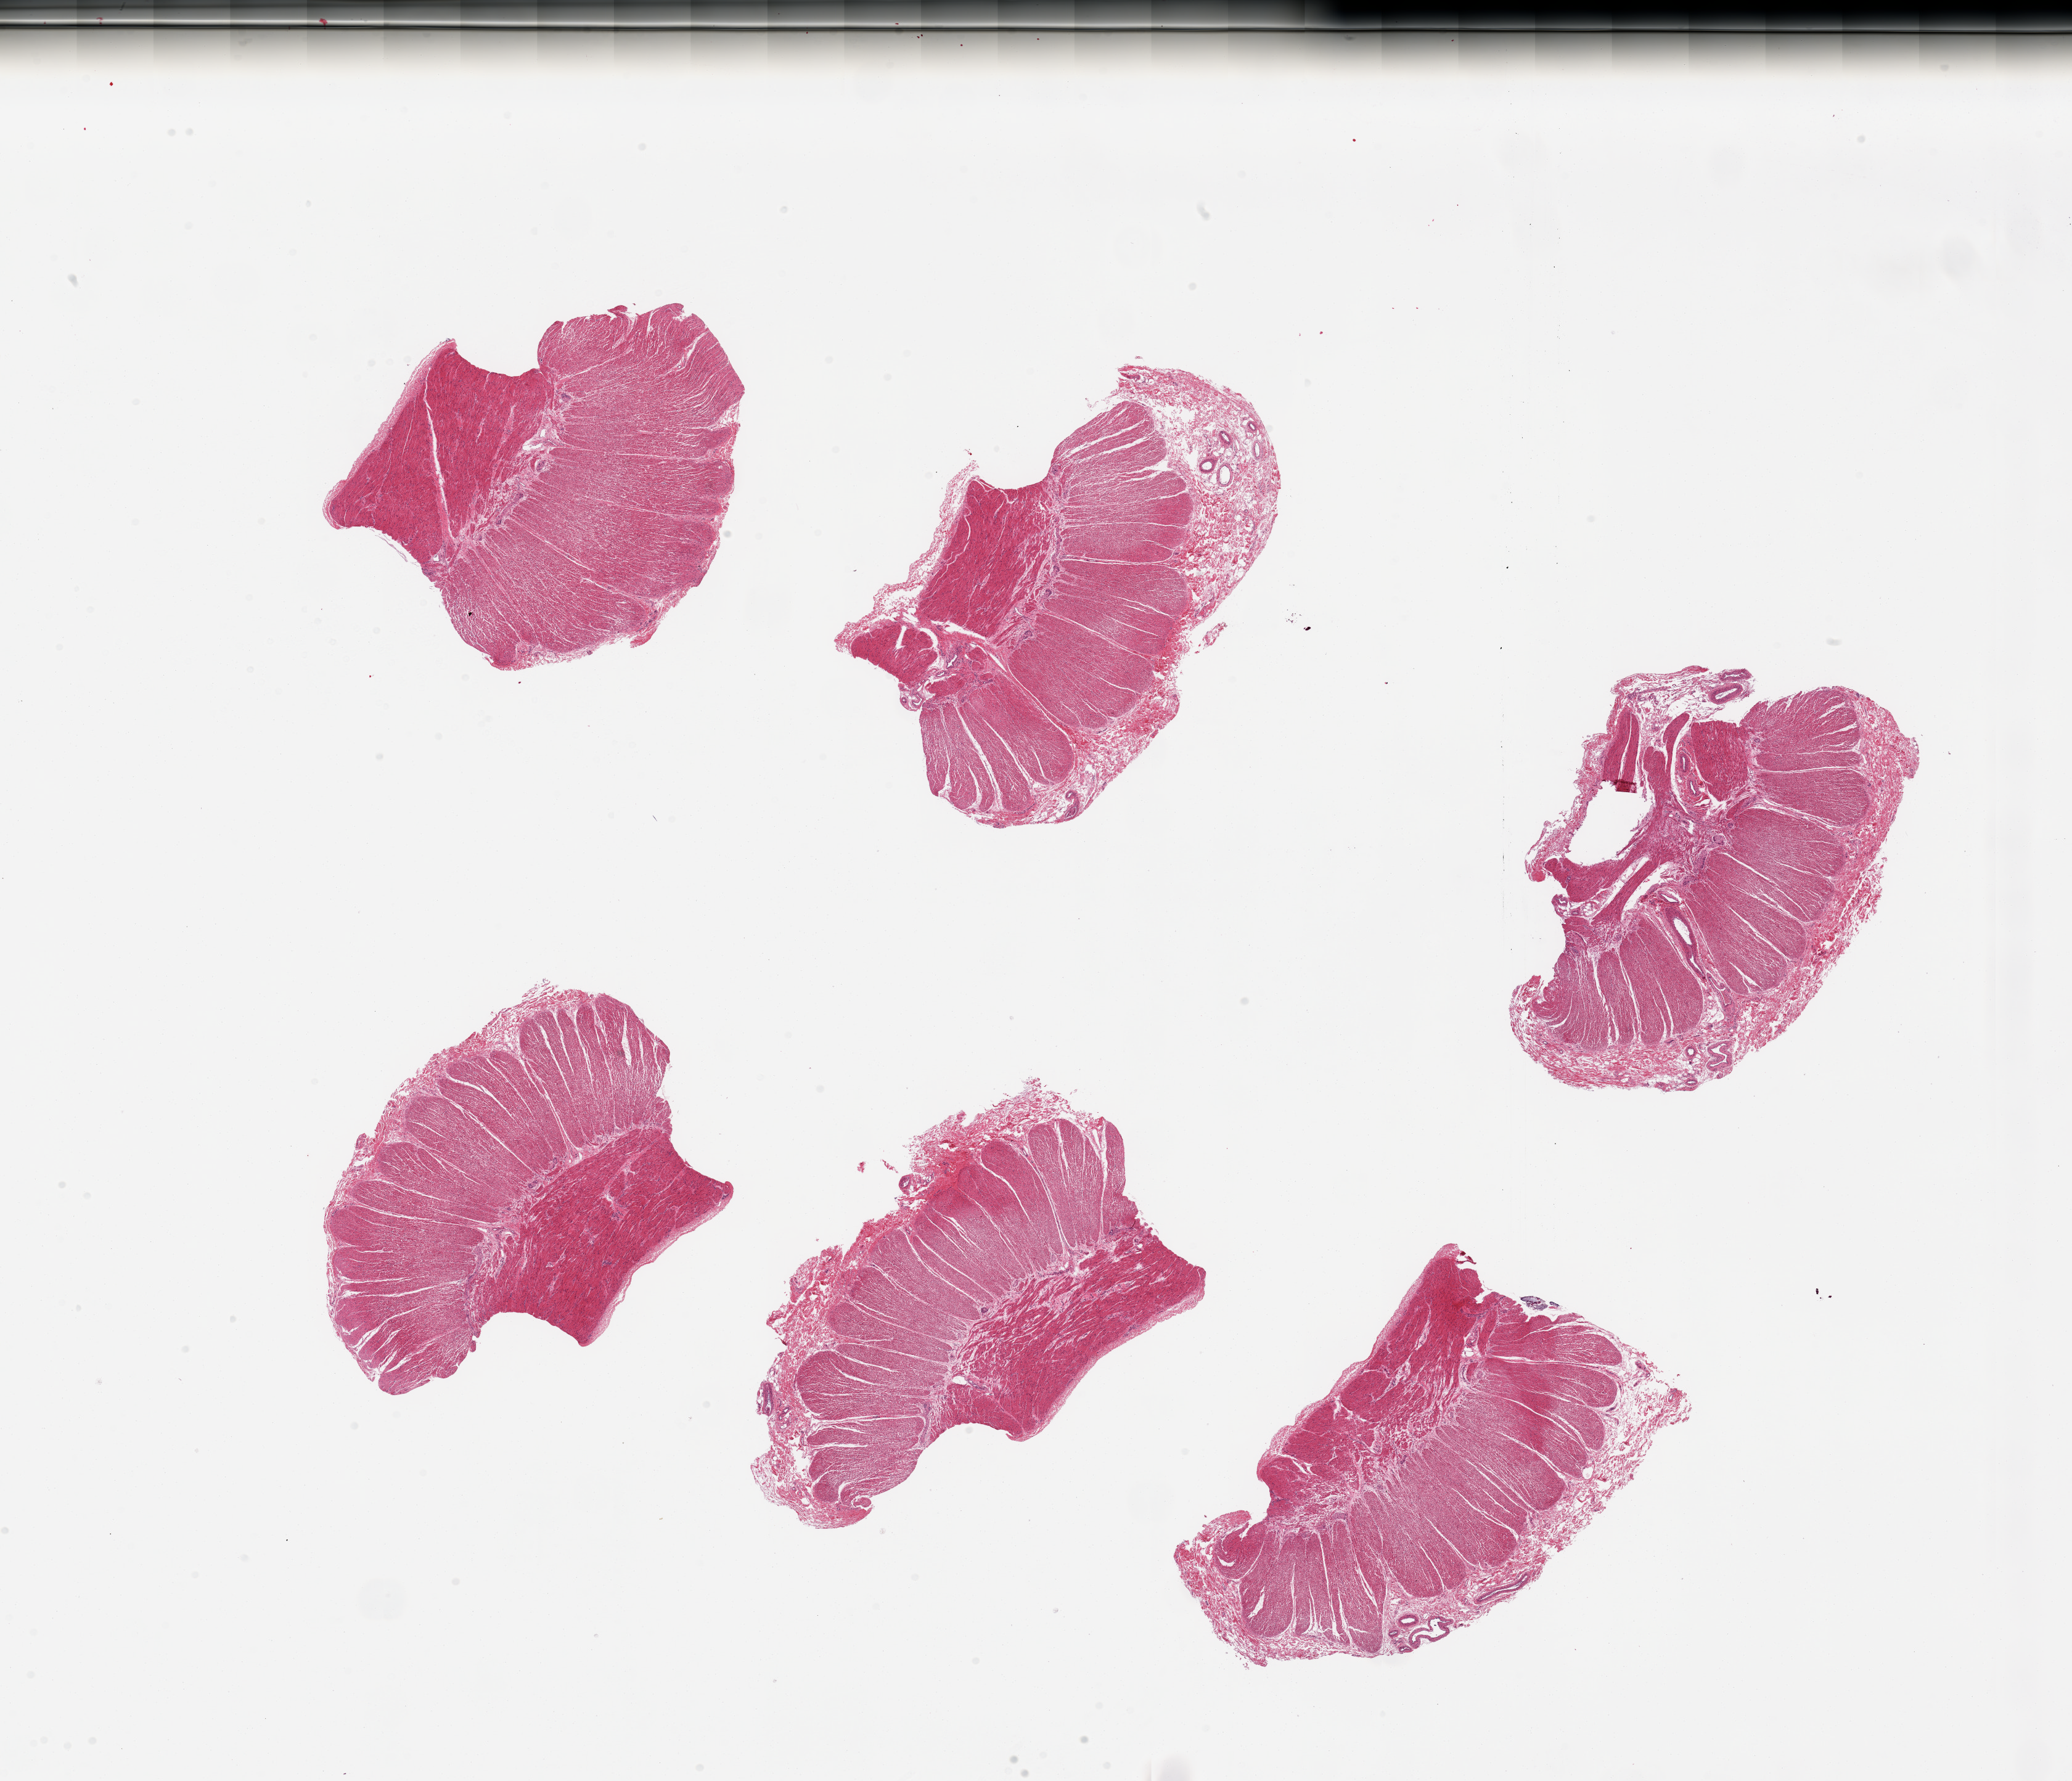
H&E whole-slide image, brightfield, whole scanned area (about 26.6 x 22.8 mm) shown as a low-resolution overview. PAXgene-fixed, paraffin-embedded tissue. Target tissue: sigmoid colon. Donor tissue sample. Male donor.
Pathologist's review note for this sample: 6 pieces, confirmed target muscularis.